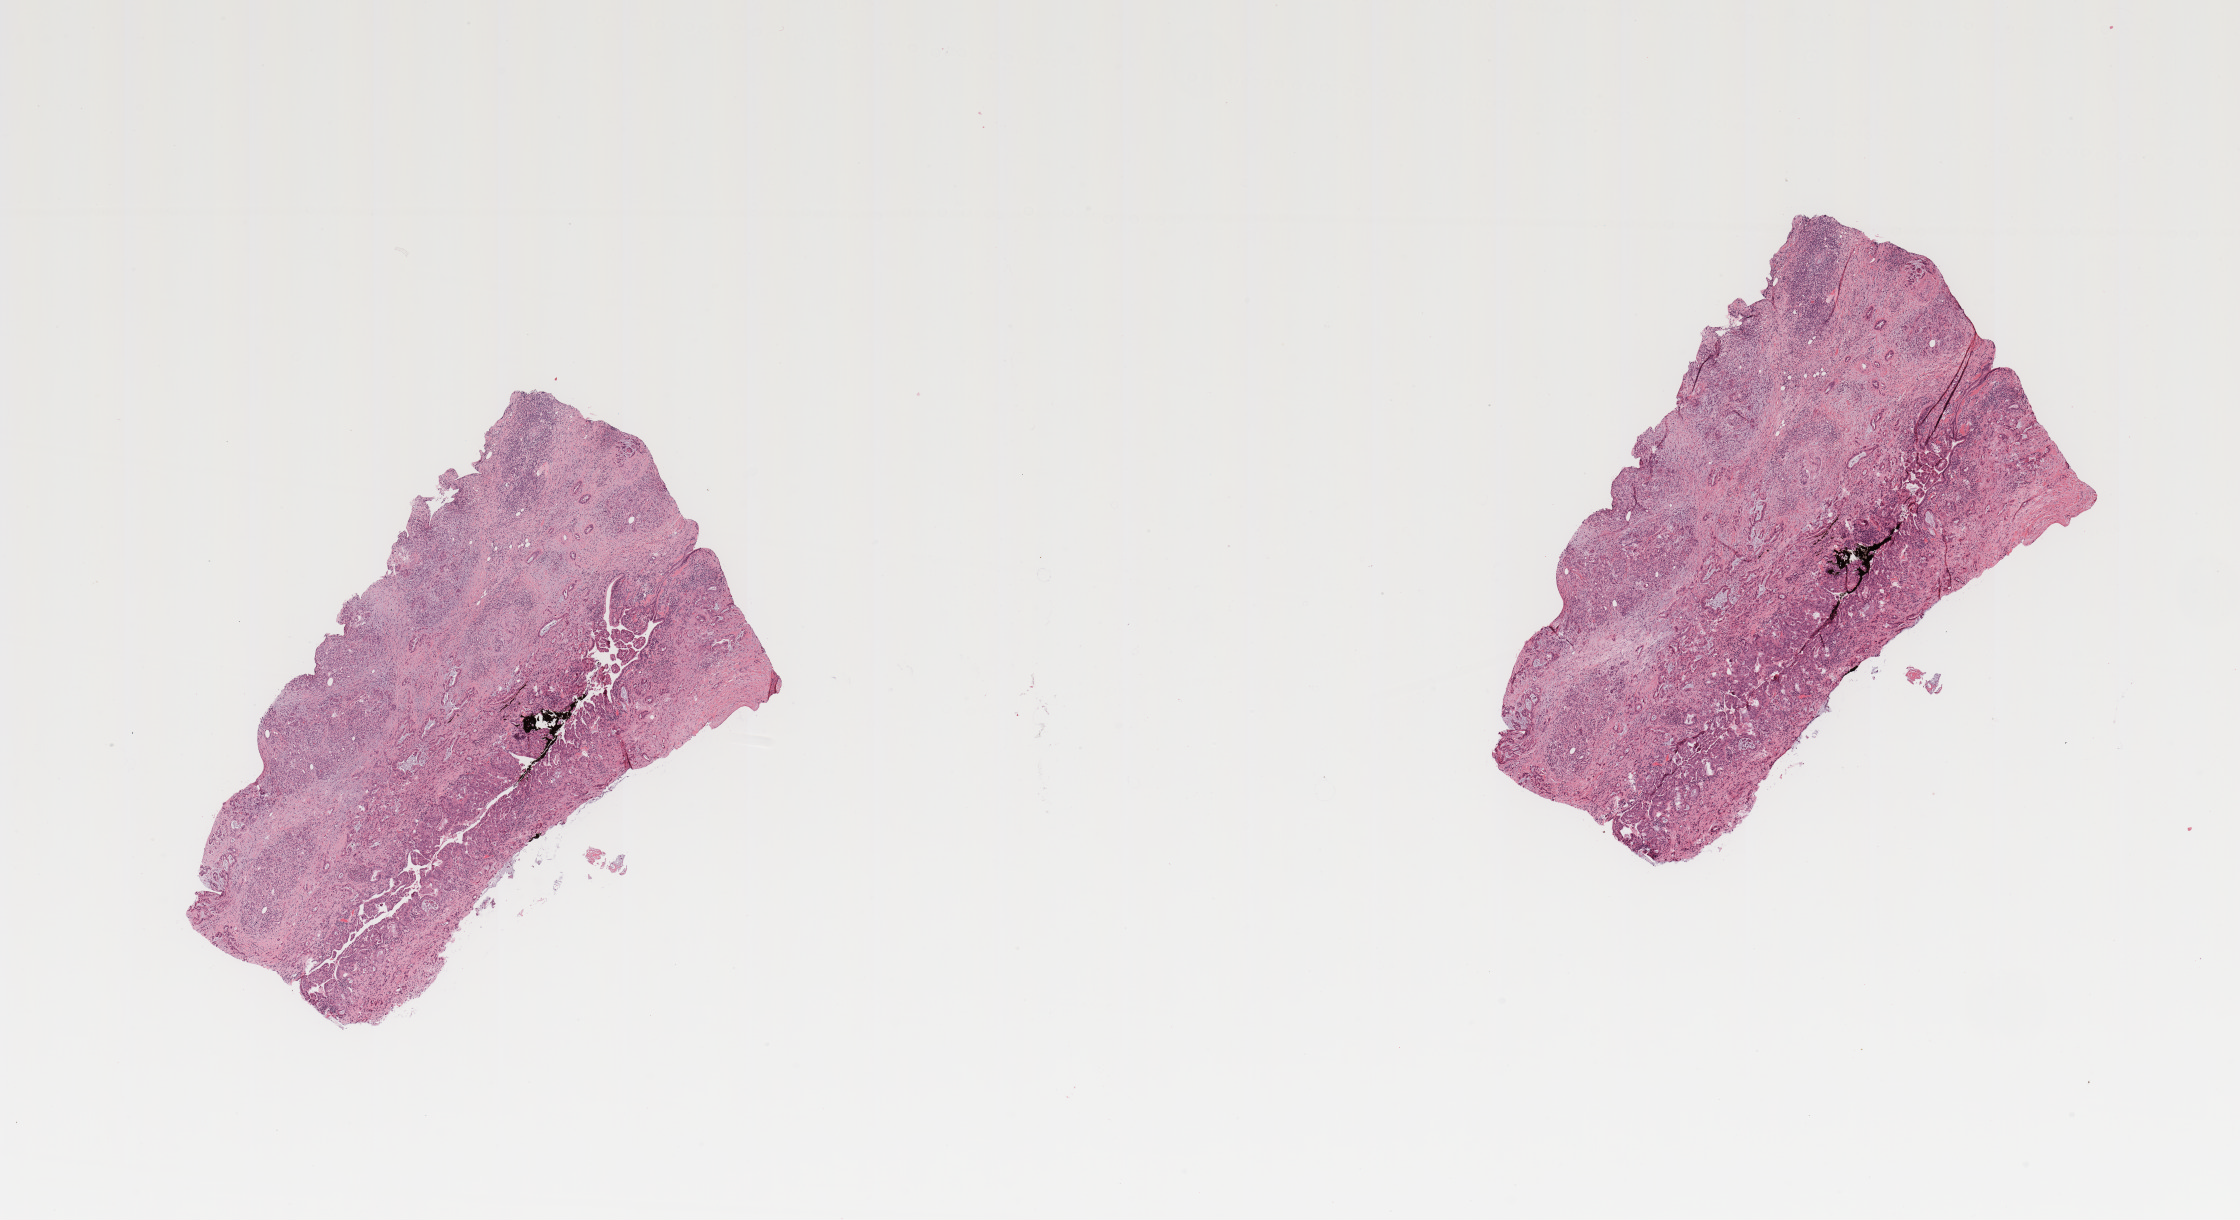
Whole-slide histology image, H&E, shown as a low-resolution overview of the whole scanned area (about 17.7 x 9.7 mm, slide scanned at 20x); tumour tissue sample, sampled site: pancreas. 67-year-old female patient. Histologic grade: G2 (moderately differentiated). Composition of this section per pathologist review: tumour nuclei 30%, necrosis 0%.
• histologic diagnosis: Infiltrating duct carcinoma, NOS
• AJCC pathologic stage: III